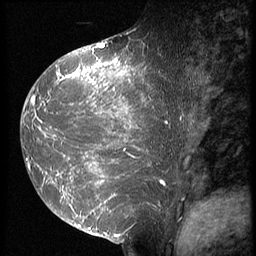
Breast MRI (dynamic contrast-enhanced), one sagittal slice; position 32 of 64 along the scan axis; 3 images stored at this slice position (order not interpretable as contrast timing); 1.5 T; TE 4.2 ms, TR 9 ms; 256 × 256 image matrix. Female patient, age 39 years. From the clinical record (not read from this slice): setting: breast cancer imaged before/during neoadjuvant chemotherapy; receptor status: HER2-positive.
Annotated regions visible in this slice (semi-automatic segmentation, software-assisted and operator-edited):
- analysis volume of interest (the breast-tissue region the enhancement analysis was run in; not a lesion): bounding box (x1, y1, x2, y2) in pixels: (23, 47, 175, 239)
- tumour enhancement mask (voxels above the 140 % enhancement threshold inside the analysis volume of interest): (23, 47, 164, 229)